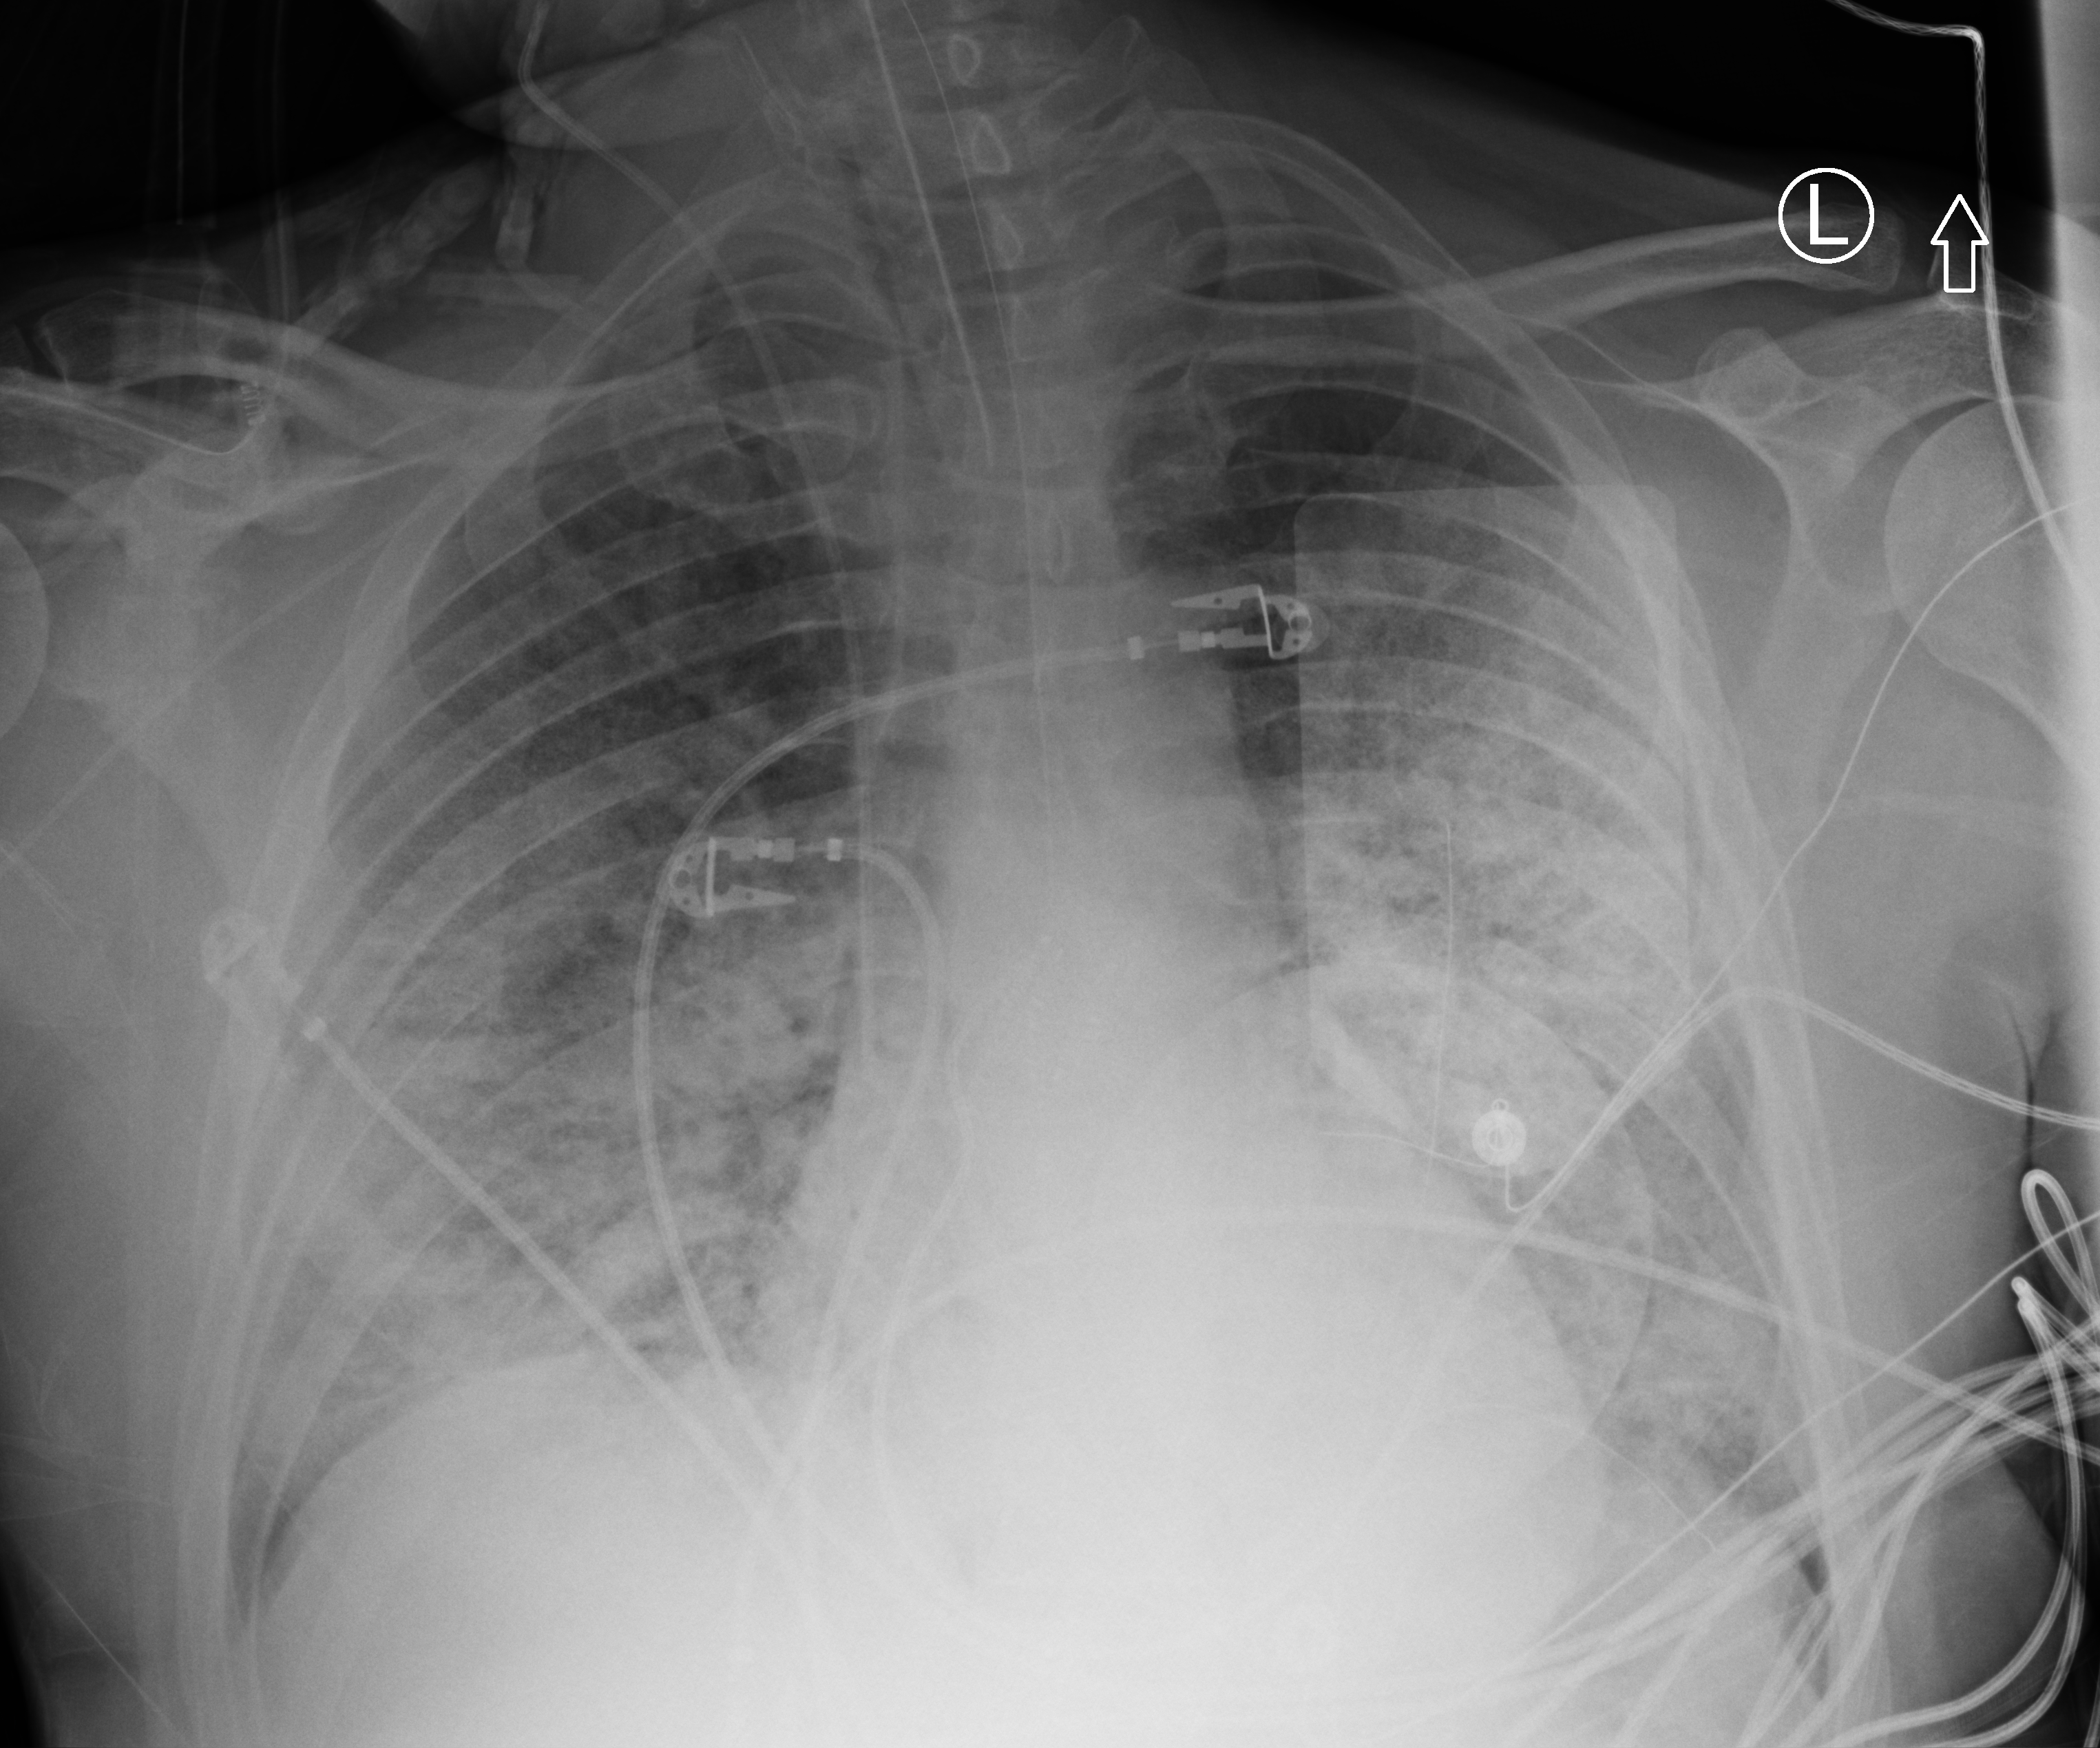
Portable chest radiograph; anteroposterior (AP) projection. Patient hospitalised with COVID-19; male, aged 18–59 years.
Admission-level facts for this patient (not findings on this image; timing relative to this image not recorded):
- length of hospital stay: 75 days
- diabetes (admission record): no